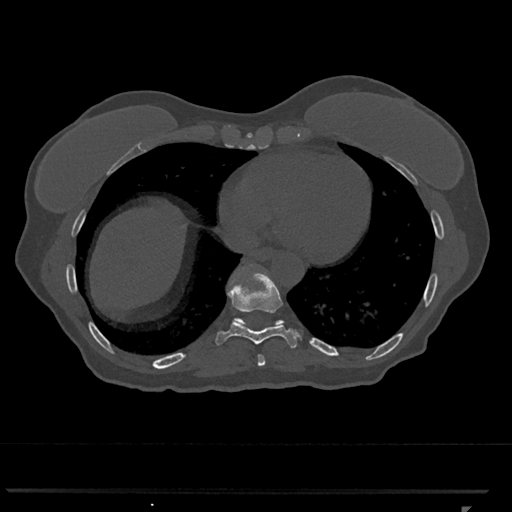
CT including the spine, one axial slice. Position 612 of 793 along the scan axis. Reconstruction kernel Br40s/3. 120 kVp. Bone window (W 1800 / L 400 HU). 512 × 512 image matrix, field of view 380 × 380 mm. Patient: female, 62 years. From the clinical record (not read from this slice): primary cancer: renal.
Structures marked on this image (semi-automatic segmentation, software-assisted and operator-edited):
- T10 vertebra: bounding box (x1, y1, x2, y2) in pixels: (235, 268, 284, 326)
- T8 vertebra: (258, 354, 266, 367)
- T9 vertebra: (215, 272, 300, 349)